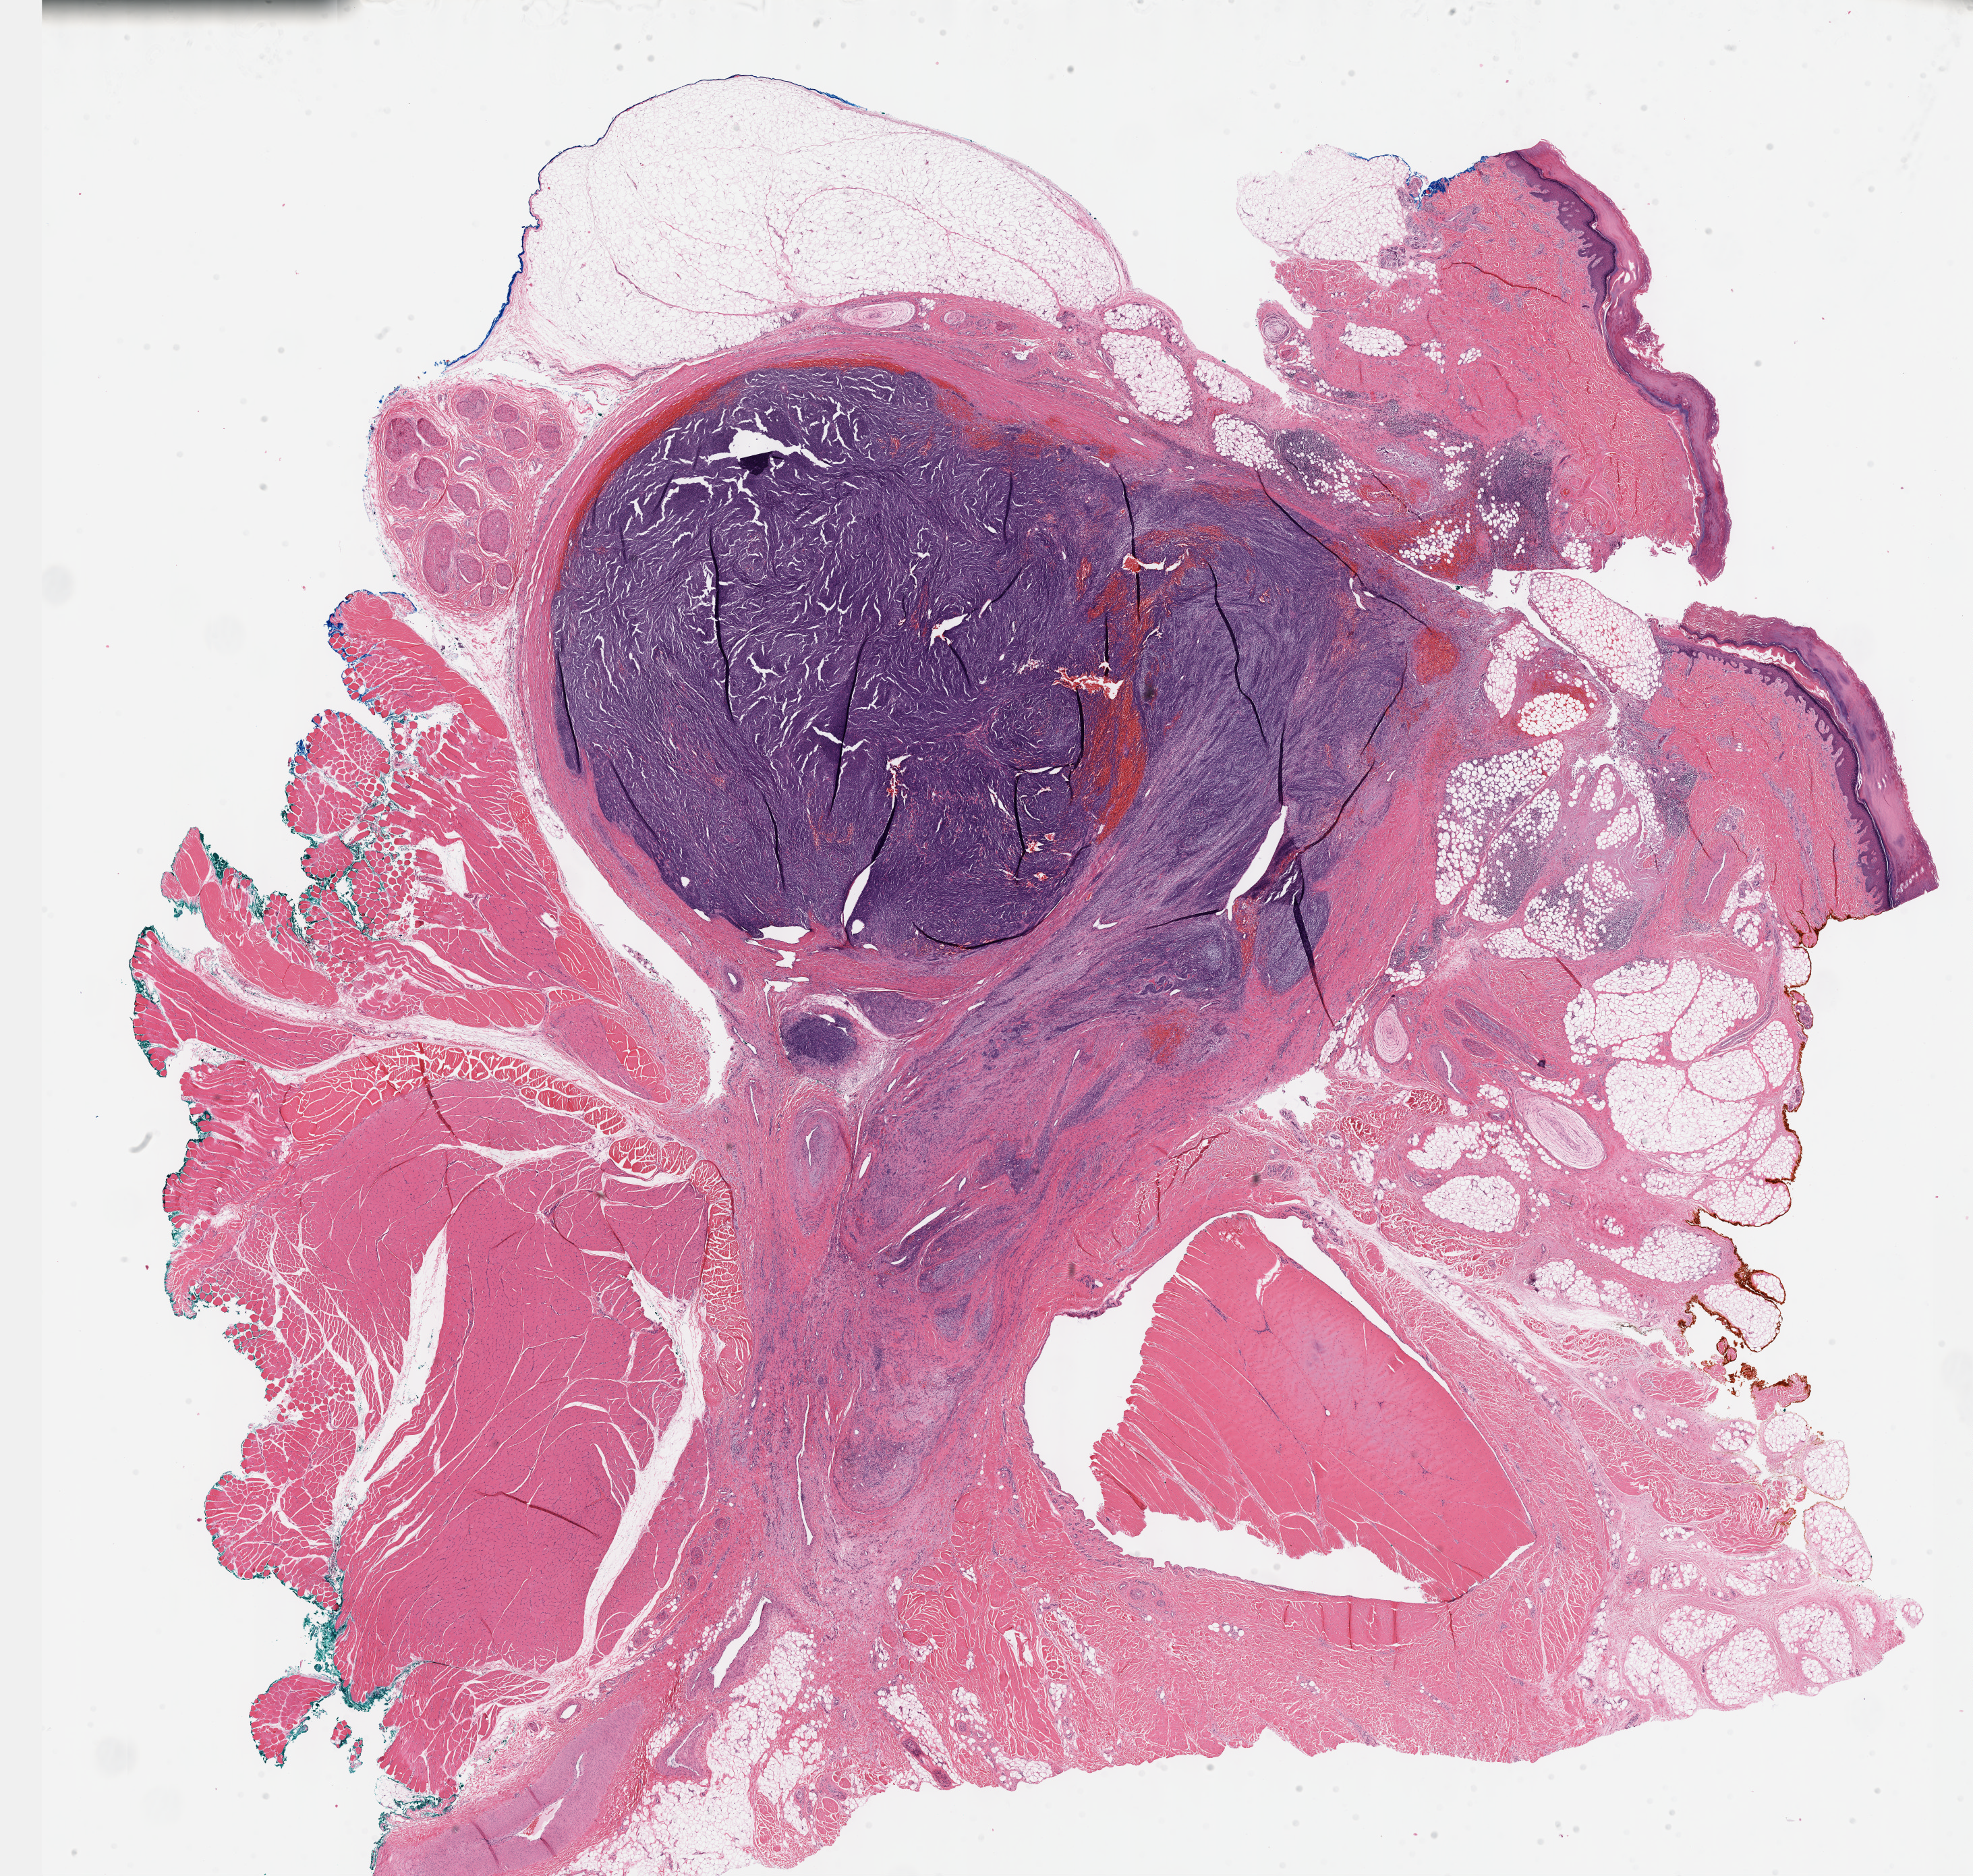
Whole-slide histology image, H&E-stained — whole scanned area (about 23.6 x 22.5 mm, acquisition: 40x scan) shown as a low-resolution overview, formalin-fixed paraffin-embedded (FFPE) diagnostic section, sample: primary tumour, connective, subcutaneous and other soft tissues. Female patient; age at initial diagnosis 24 years.
* histologic diagnosis: Synovial sarcoma, biphasic (connective, subcutaneous and other soft tissues of lower limb and hip)